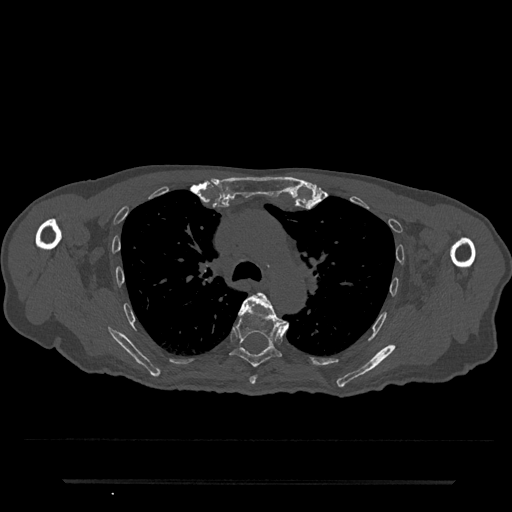
CT including the spine, one axial slice; position 539 of 797 along the scan axis; reconstruction kernel Br40s/3; bone window (W 1800 / L 400 HU); 0.5 mm slice thickness; 512 × 512 image matrix, field of view 427 × 427 mm. Patient: male, 74 years. From the clinical record (not read from this slice): primary cancer: prostate.
Structures marked on this image (semi-automatic segmentation, software-assisted and operator-edited):
- T5 vertebra: bounding box (x1, y1, x2, y2) in pixels: (240, 293, 289, 385)
- T6 vertebra: (230, 293, 282, 367)